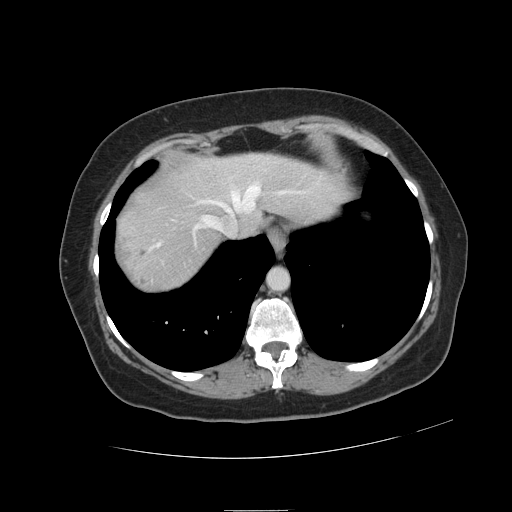
Contrast-enhanced abdominal CT, one axial slice; slice 103 of 121 in the series (ordered by position); 120 kVp; intravenous contrast given; soft-tissue window (W 400 / L 40 HU); 2.5 mm slice thickness; 512 × 512 image matrix, field of view 400 × 400 mm. Female patient, age 52 years. Case-level facts recorded for this patient, not image findings: diagnosis: colorectal cancer liver metastases, imaged before liver resection; multiple liver metastases: yes; largest metastasis: 6.3 cm; chemotherapy before resection: yes.
Outlined on this slice (outlined manually by an expert reader):
- hepatic veins: bounding box <149,184,308,250> (left, top, right, bottom; pixels)
- liver: <115,154,345,292>
- planned liver remnant (the part of the liver to remain after resection): <180,154,342,230>